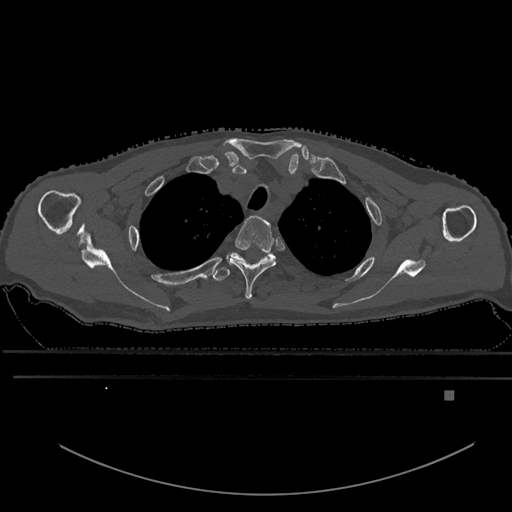
CT including the spine, one axial slice; position 485 of 969 along the scan axis; bone window (W 1800 / L 400 HU); 0.5 mm slice thickness; 512 × 512 image matrix. Male patient, age 82 years. From the clinical record (not read from this slice): primary cancer: prostate; vertebrae with lytic lesions (as recorded): T11, T9, T8, T2.
Structures marked on this image (semi-automatic segmentation, software-assisted and operator-edited):
- T2 vertebra: bounding box <226,215,277,300> (left, top, right, bottom; pixels)
- T3 vertebra: <212,253,269,282>